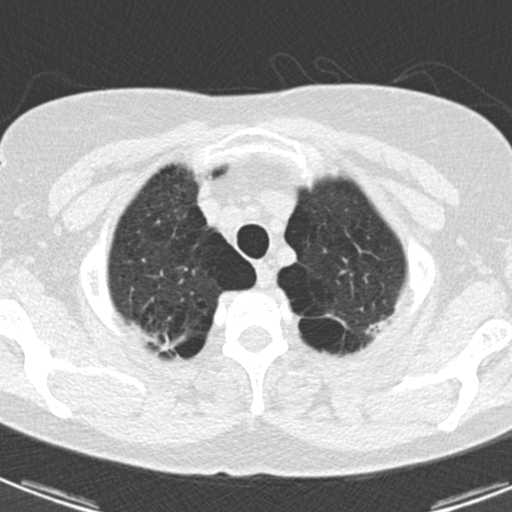
Low-dose screening chest CT, axial slice; third annual screen; lung window (W 1500 / L -600 HU); 2 mm slice thickness; slice 19 of 174 in the series. Female, age 59 years at enrolment.
- Expert reader's lesion annotation, bounding box <130,319,186,364> (left, top, right, bottom; pixels).
- Screening reader's record for this exam (one nodule recorded; not confirmed to be the boxed lesion): non-calcified nodule or mass ≥4 mm, right upper lobe, 12 × 7 mm, spiculated (stellate) margins, soft tissue attenuation, pre-existing on the prior screen: yes; interval growth: yes.